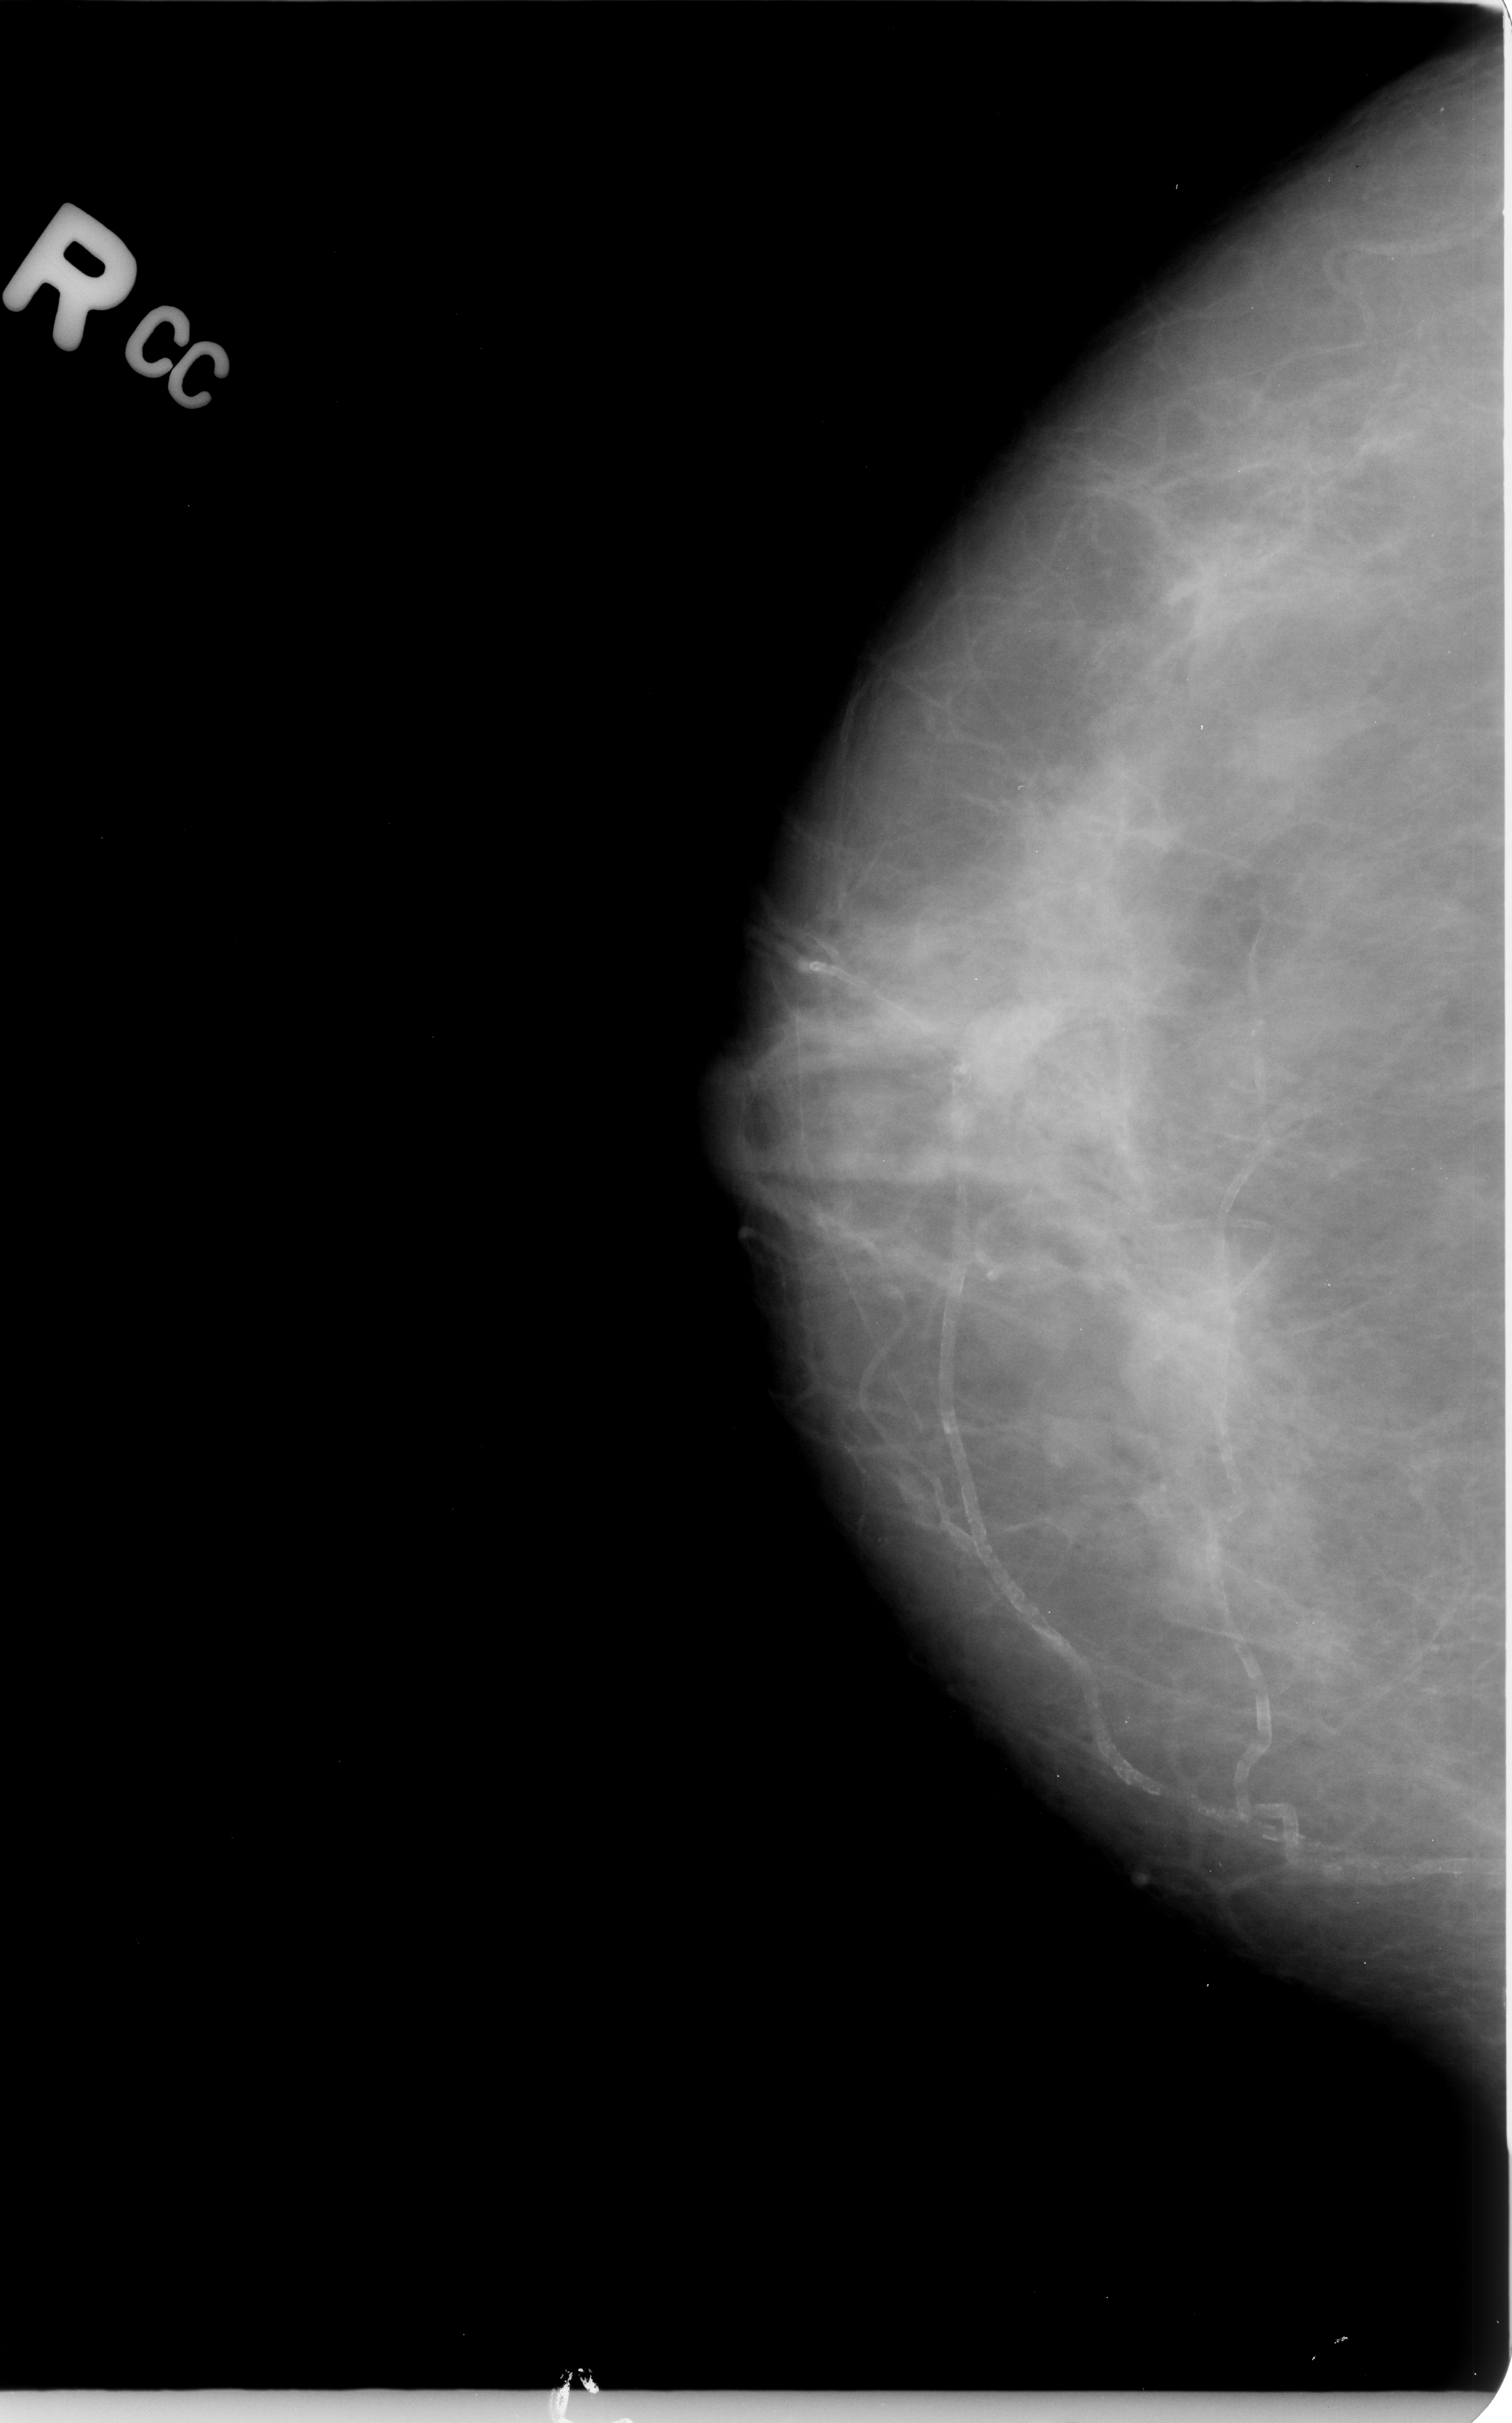
Mammogram (digitized film); right breast; CC view; BI-RADS breast density category 3 (scale 1–4).
Mass, shape irregular, margins obscured / ill defined; BI-RADS assessment category 4; pathology (as recorded): malignant.